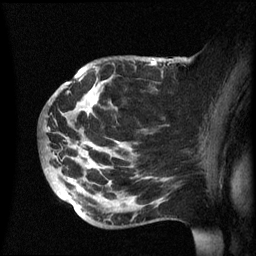
Breast MRI (dynamic contrast-enhanced), one sagittal slice; slice 38 of 60 in the series (ordered by position); dynamic contrast-enhanced series, image 2 of 3 at this slice position (ordered by acquisition); 1.5 T; TE 4.2 ms, TR 8.4 ms; 256 × 256 image matrix. Female patient, age 49 years.
Outlined on this slice (semi-automatic segmentation, software-assisted and operator-edited):
- analysis volume of interest (the breast-tissue region the enhancement analysis was run in; not a lesion): box from (x=43, y=56) to (x=174, y=228) px
- tumour enhancement mask (voxels above the 70 % enhancement threshold inside the analysis volume of interest): (x=72, y=62)–(x=156, y=184)